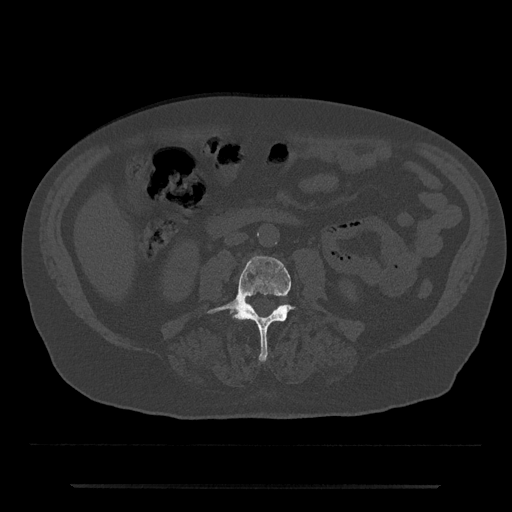
CT including the spine, one axial slice. Position 406 of 797 along the scan axis. 120 kVp. Bone window (W 1800 / L 400 HU). 0.5 mm slice thickness. 512 × 512 image matrix. Male patient, age 80 years. From the clinical record (not read from this slice): primary cancer: prostate.
Annotated regions visible in this slice (semi-automatic segmentation, software-assisted and operator-edited):
- L3 vertebra: bounding box (x1, y1, x2, y2) in pixels: (208, 256, 295, 362)
- L4 vertebra: (234, 315, 236, 317)